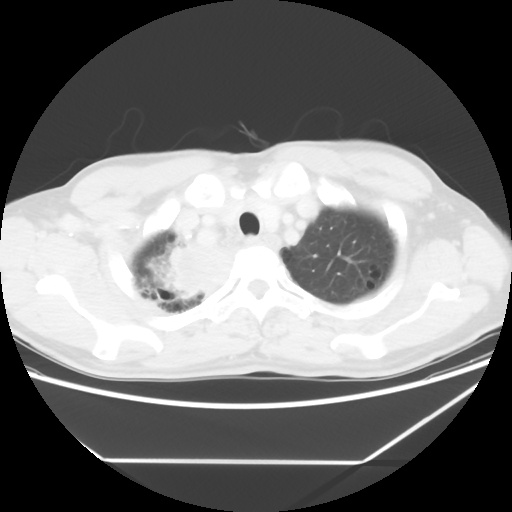
Chest CT, one axial slice; position 53 of 60 along the scan axis; lung window (W 1500 / L -600 HU); 5 mm slice thickness; 512 × 512 image matrix, field of view 367 × 367 mm. Male patient, age 58 years. From the clinical record (not read from this slice): clinical TNM (as recorded): T2 N2 M0.
Structures marked on this image (rectangle marked by the reading radiologist):
- lung tumour (recorded histology: squamous cell carcinoma): bounding box <157,245,234,305> (left, top, right, bottom; pixels)